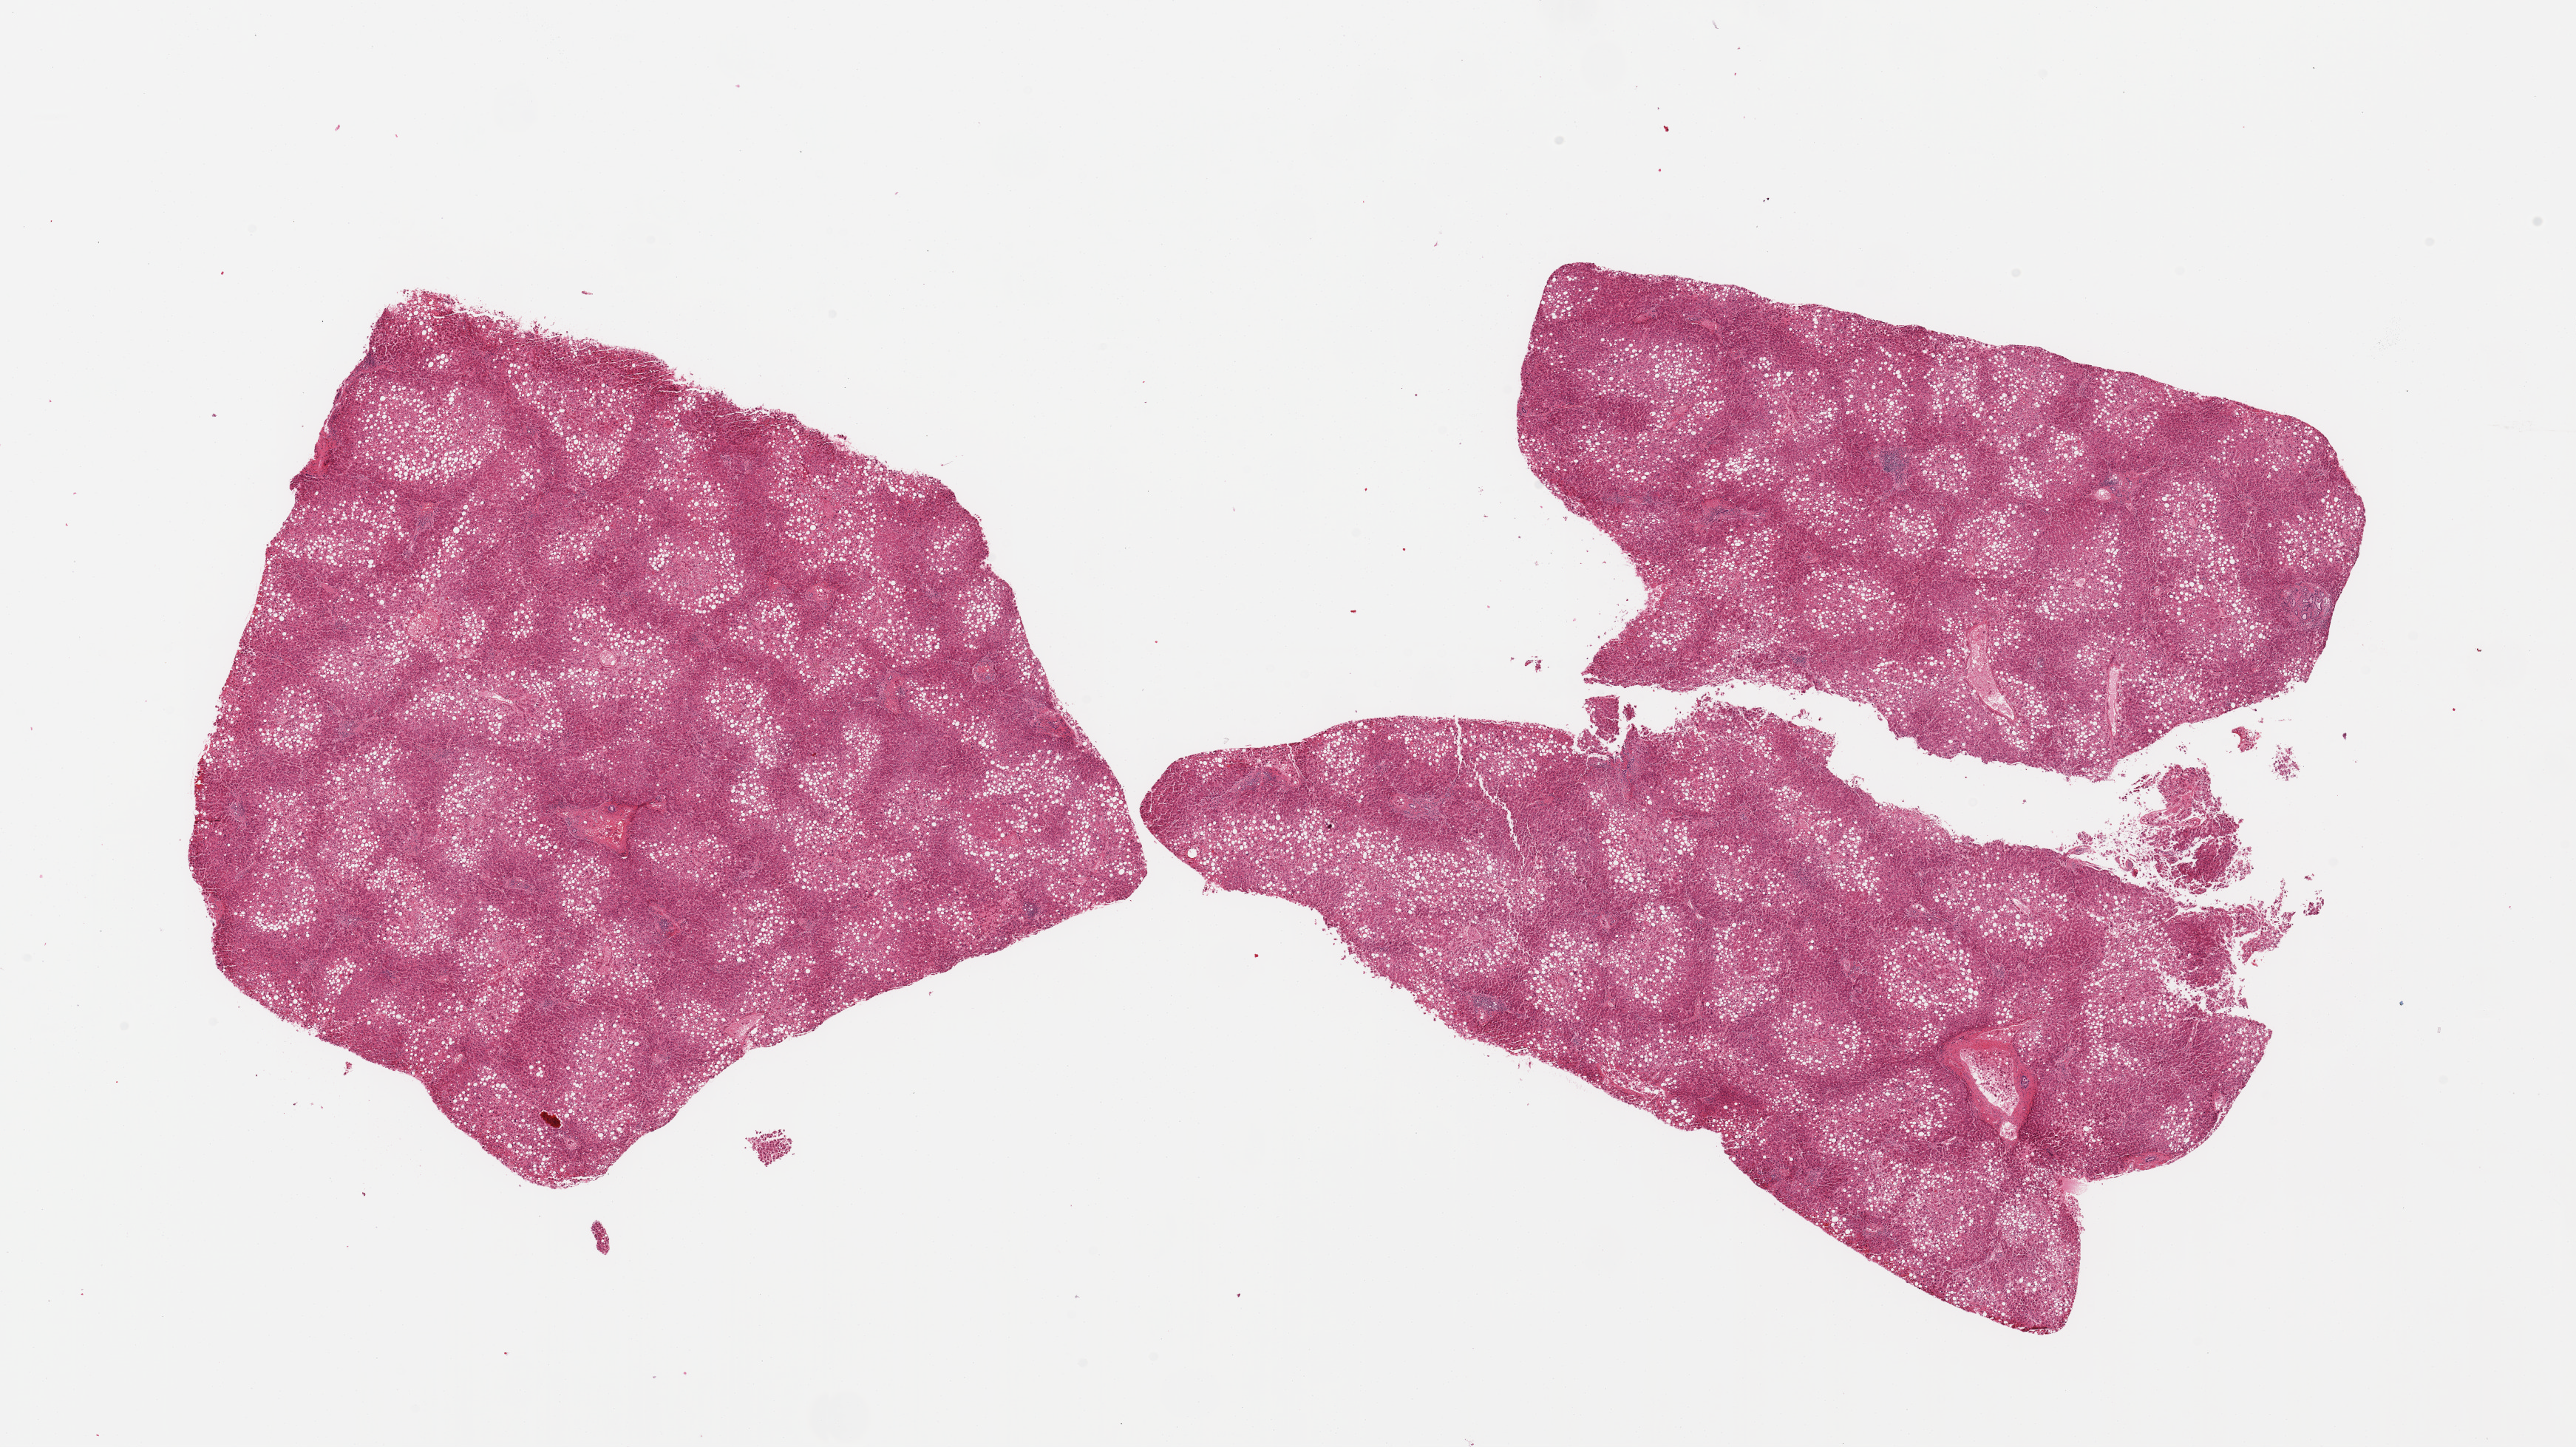
Digitized haematoxylin and eosin-stained section, brightfield — whole scanned area (about 27.6 x 15.5 mm, slide scanned at 20x) shown as a low-resolution overview; PAXgene-fixed paraffin-embedded (PFPE) section; section of liver (target tissue); donor tissue sample. Donor: male.
* reviewer comment on this tissue sample: 2 pieces, macrovesicular steatosis involves ~60-70% of parenchyma; moderate passive congestion